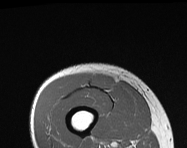
MRI of an extremity soft-tissue mass, one axial slice. MR volume resampled by the dataset authors to the PET/CT grid (not the native acquisition matrix). 3.27 mm slice thickness. 187 × 148 image matrix, field of view 183 × 145 mm. Male patient. From the clinical record (not read from this slice): histological type: pleiomorphic leiomyosarcoma; grade: intermediate; site of the primary tumour: right thigh.
Structures marked on this image (expert contour drawn on MRI and transferred to this co-registered scan by the dataset authors):
- gross tumour volume including surrounding oedema: box from (x=89, y=72) to (x=115, y=91) px